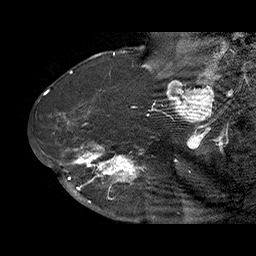
Breast MRI (dynamic contrast-enhanced), one sagittal slice; position 44 of 70 along the scan axis; dynamic contrast-enhanced series, time point 2 of 6 at this slice position (early post-contrast); 1.5 T; TE 4.5 ms, TR 32.4 ms; 256 × 256 image matrix, field of view 180 × 180 mm. Female patient. Case-level facts recorded for this patient, not image findings: setting: breast cancer imaged before/during neoadjuvant chemotherapy; receptor status: HR-positive, HER2-negative.
Structures marked on this image (semi-automatic segmentation, software-assisted and operator-edited):
- analysis volume of interest (the breast-tissue region the enhancement analysis was run in; not a lesion): box from (x=71, y=128) to (x=159, y=202) px
- tumour enhancement mask (voxels above the 100 % enhancement threshold inside the analysis volume of interest): (x=71, y=142)–(x=147, y=202)